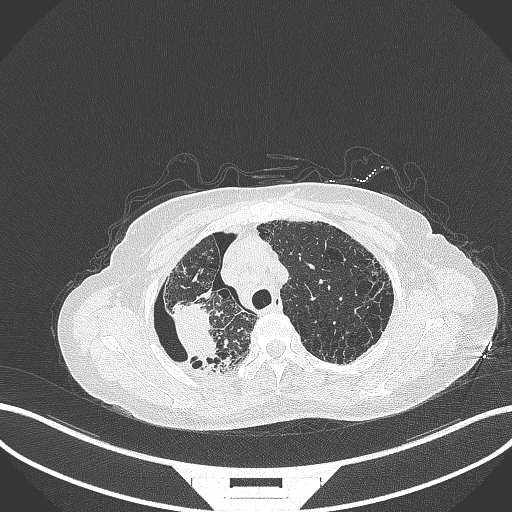
Chest CT, one axial slice; position 281 of 408 along the scan axis; reconstruction kernel B70f; lung window (W 1500 / L -600 HU); 1 mm slice thickness; 512 × 512 image matrix, field of view 400 × 400 mm. Female patient, age 64 years. From the clinical record (not read from this slice): clinical TNM (as recorded): T3 N3 M0.
Annotated regions visible in this slice (rectangle marked by the reading radiologist):
- lung tumour (recorded histology: squamous cell carcinoma): bounding box (x1, y1, x2, y2) in pixels: (168, 296, 229, 369)